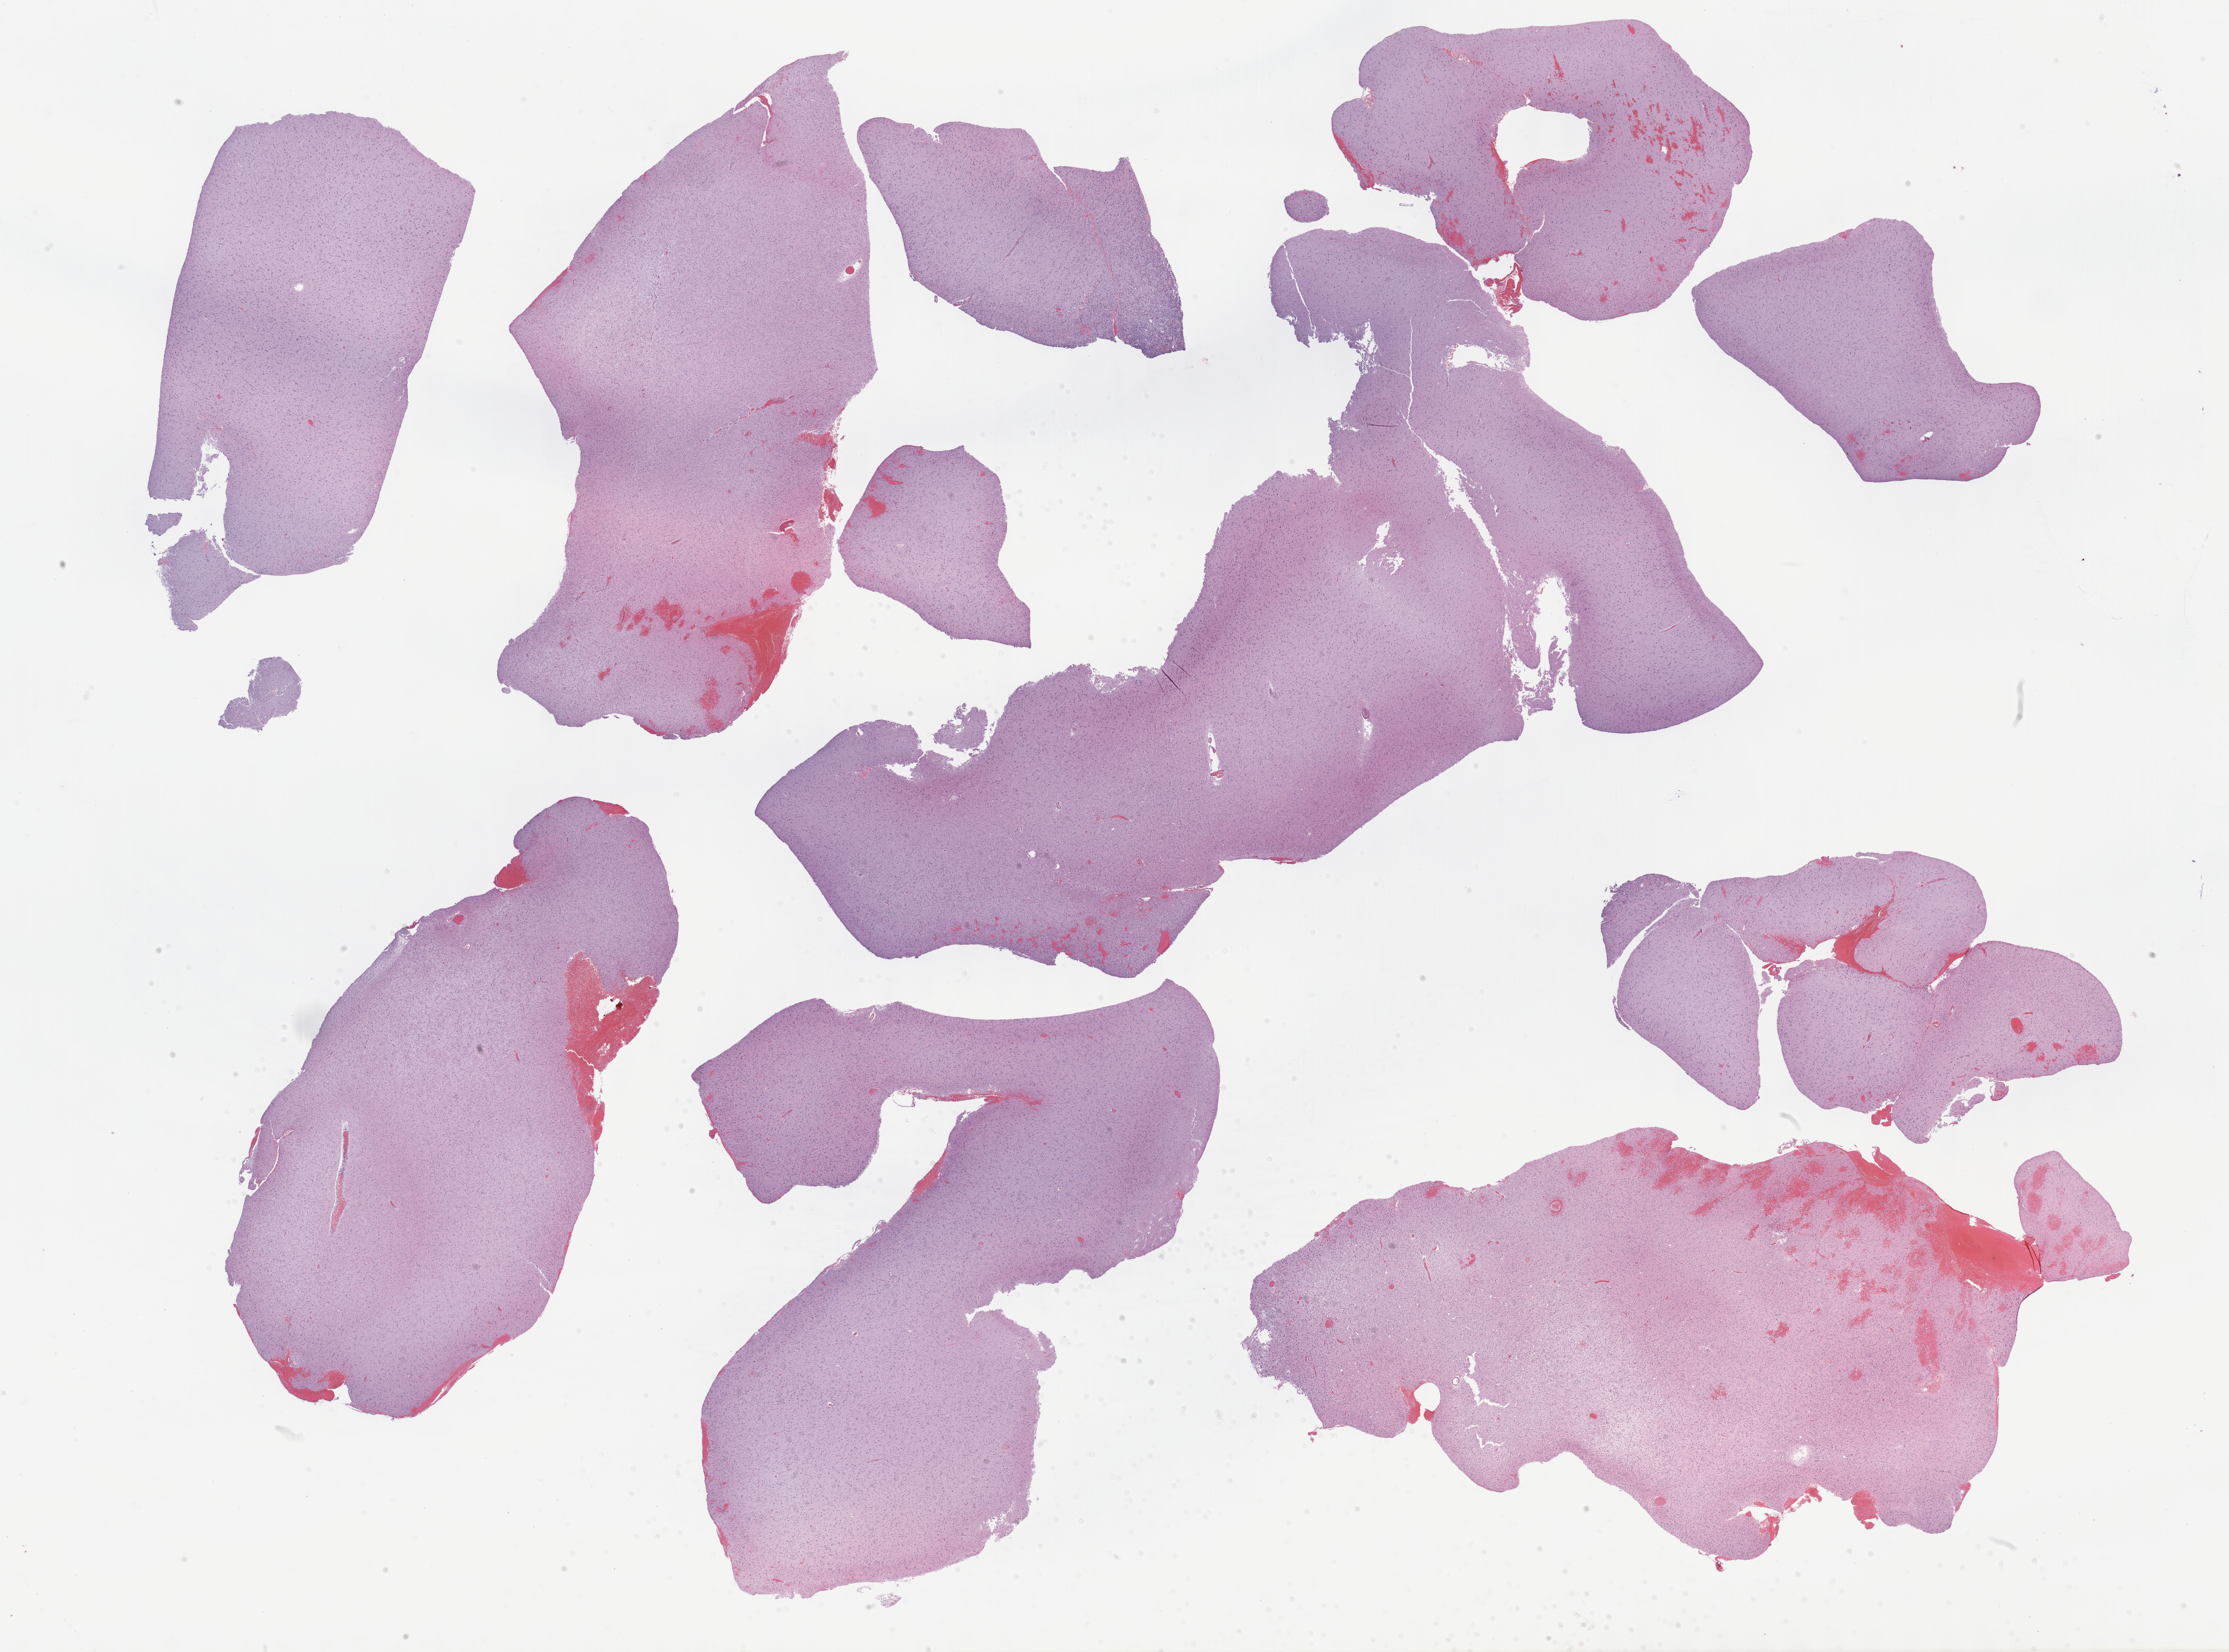
Digitized H&E-stained tissue section (whole slide), a low-resolution overview of the entire scanned area, about 29.7 x 22.0 mm (slide scanned at 40x), formalin-fixed paraffin-embedded (FFPE) diagnostic section, brain, primary tumour sample. Patient: male, age at initial diagnosis 54 years. Histologic grade: G2 (moderately differentiated).
Pathologic diagnosis: Oligodendroglioma, NOS (cerebrum).